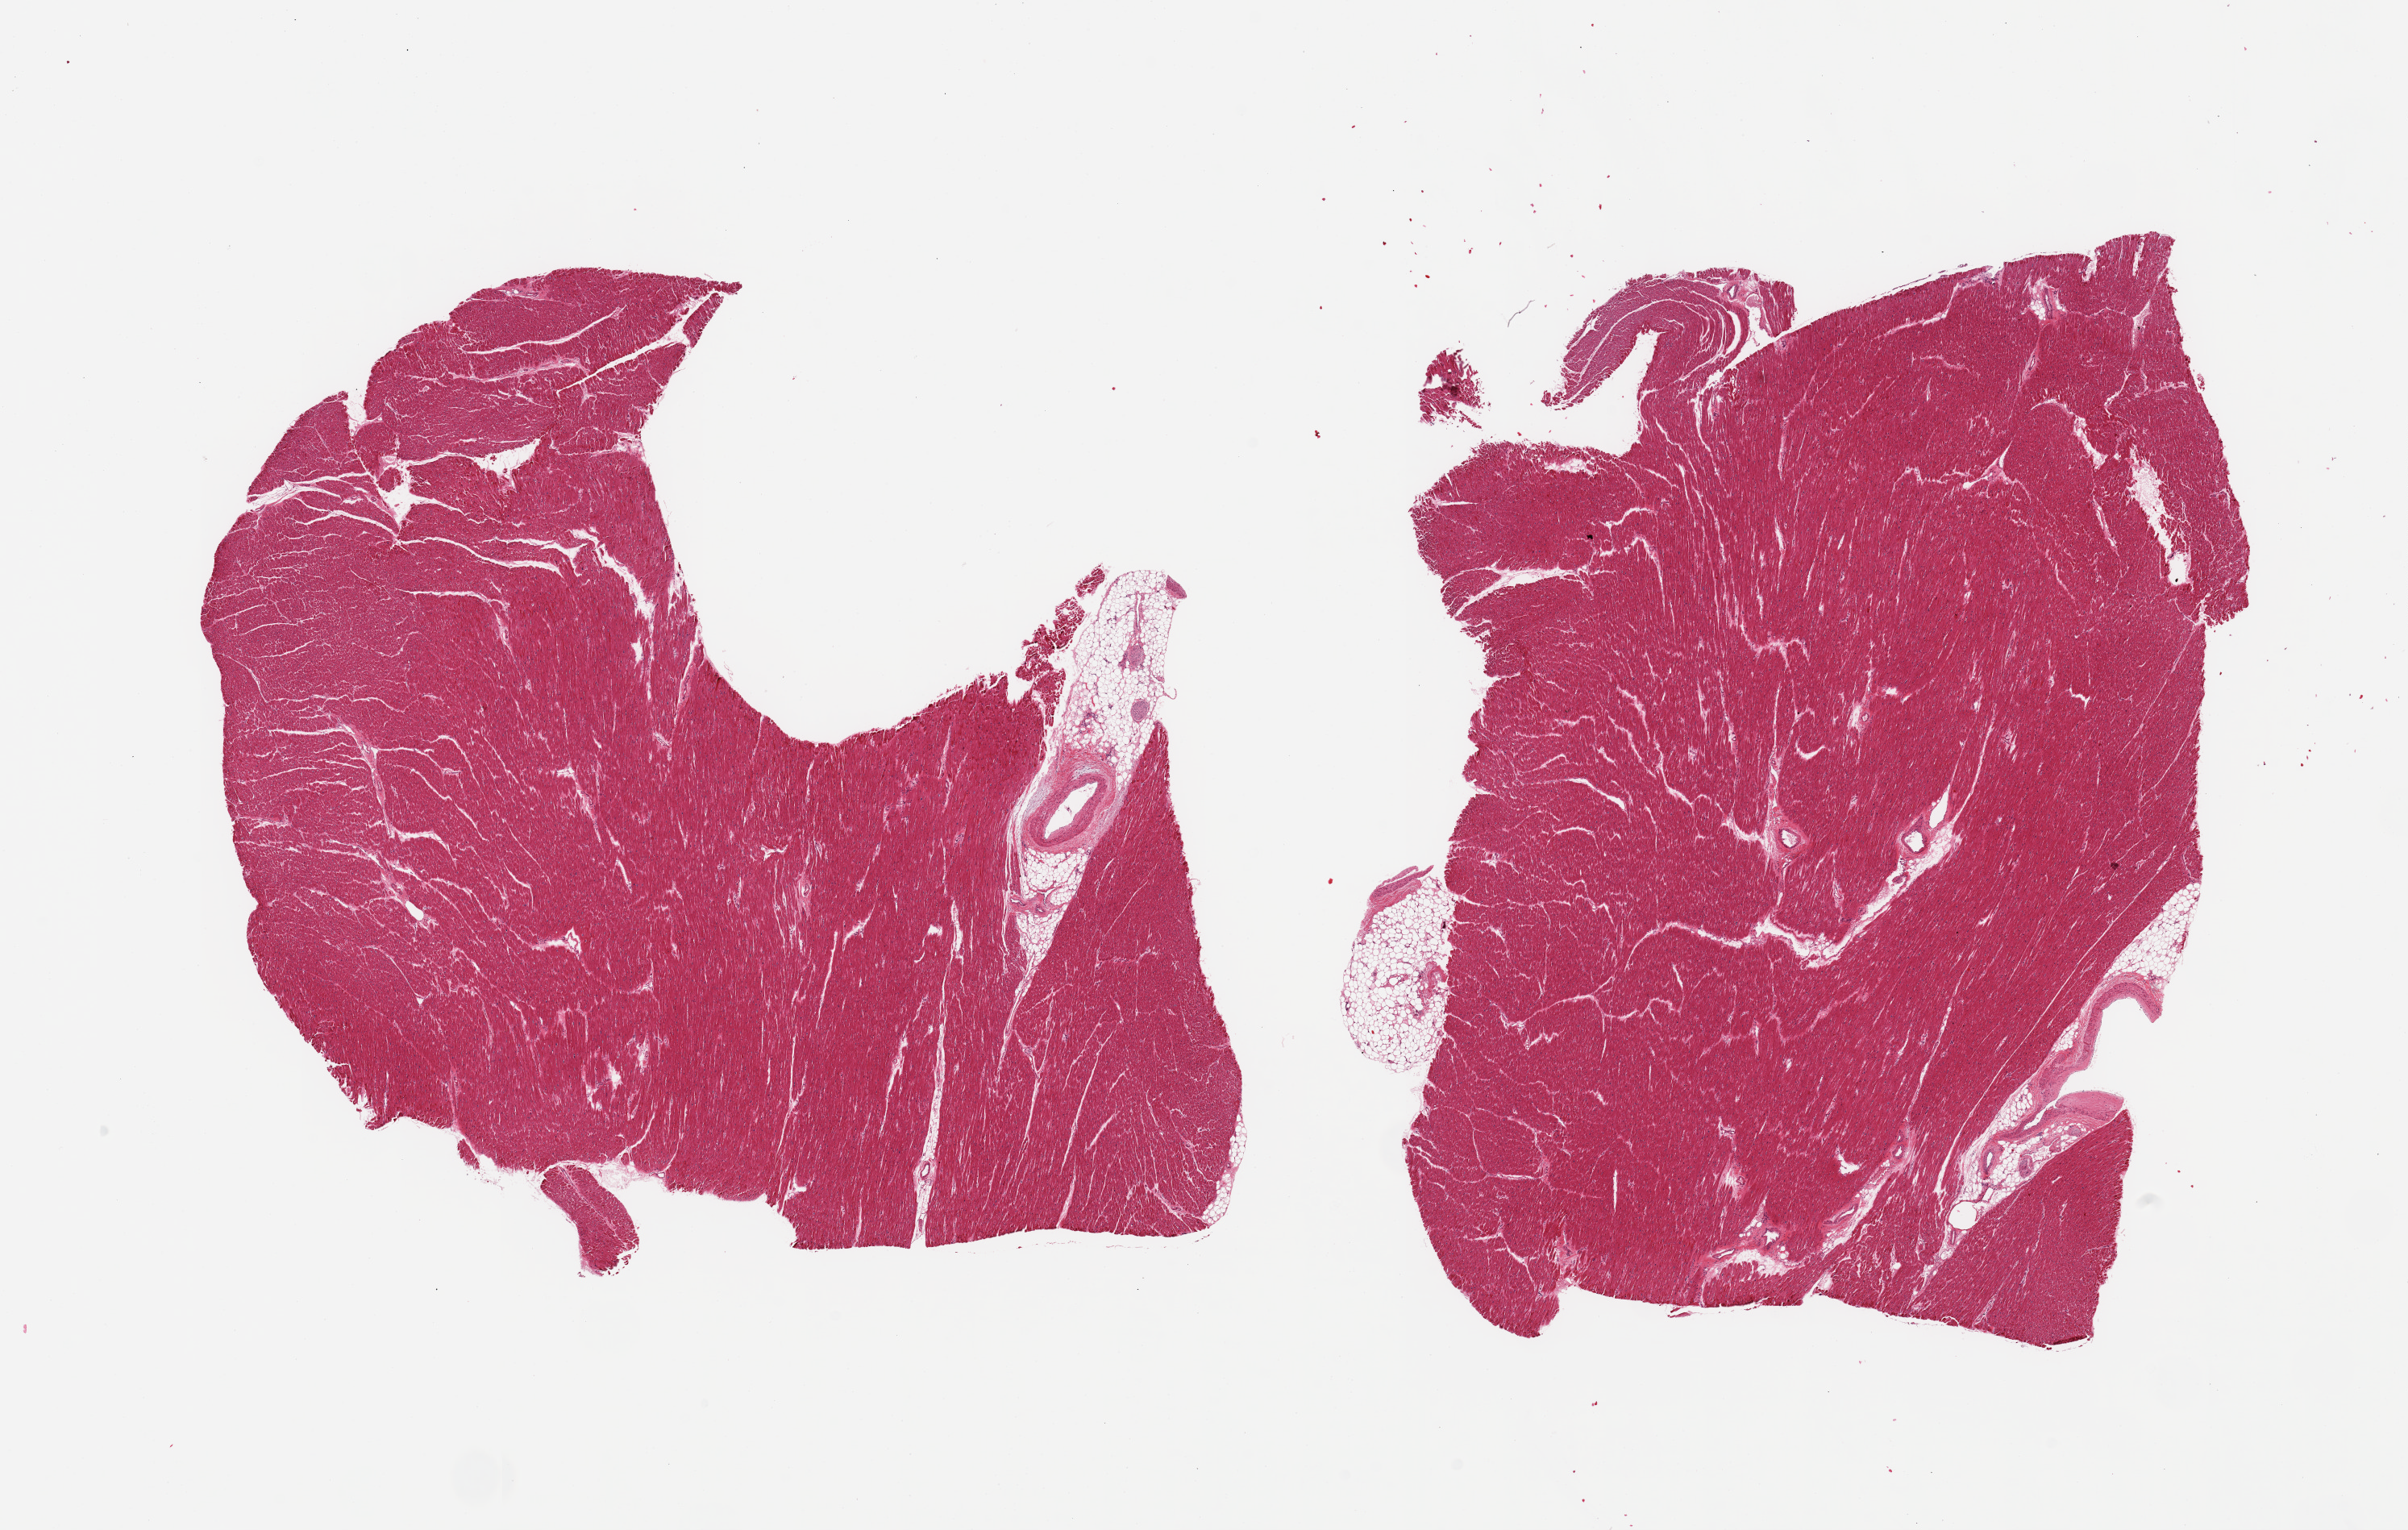
Digitized H&E-stained section, a low-resolution overview of the entire scanned area, about 23.6 x 15.0 mm. PAXgene-fixed paraffin-embedded (PFPE) section. Sampled site (target tissue): heart. Tissue donor sample. Donor: female.
Review note (as recorded): 2 pieces, no significant ischemic damage, trace fat.